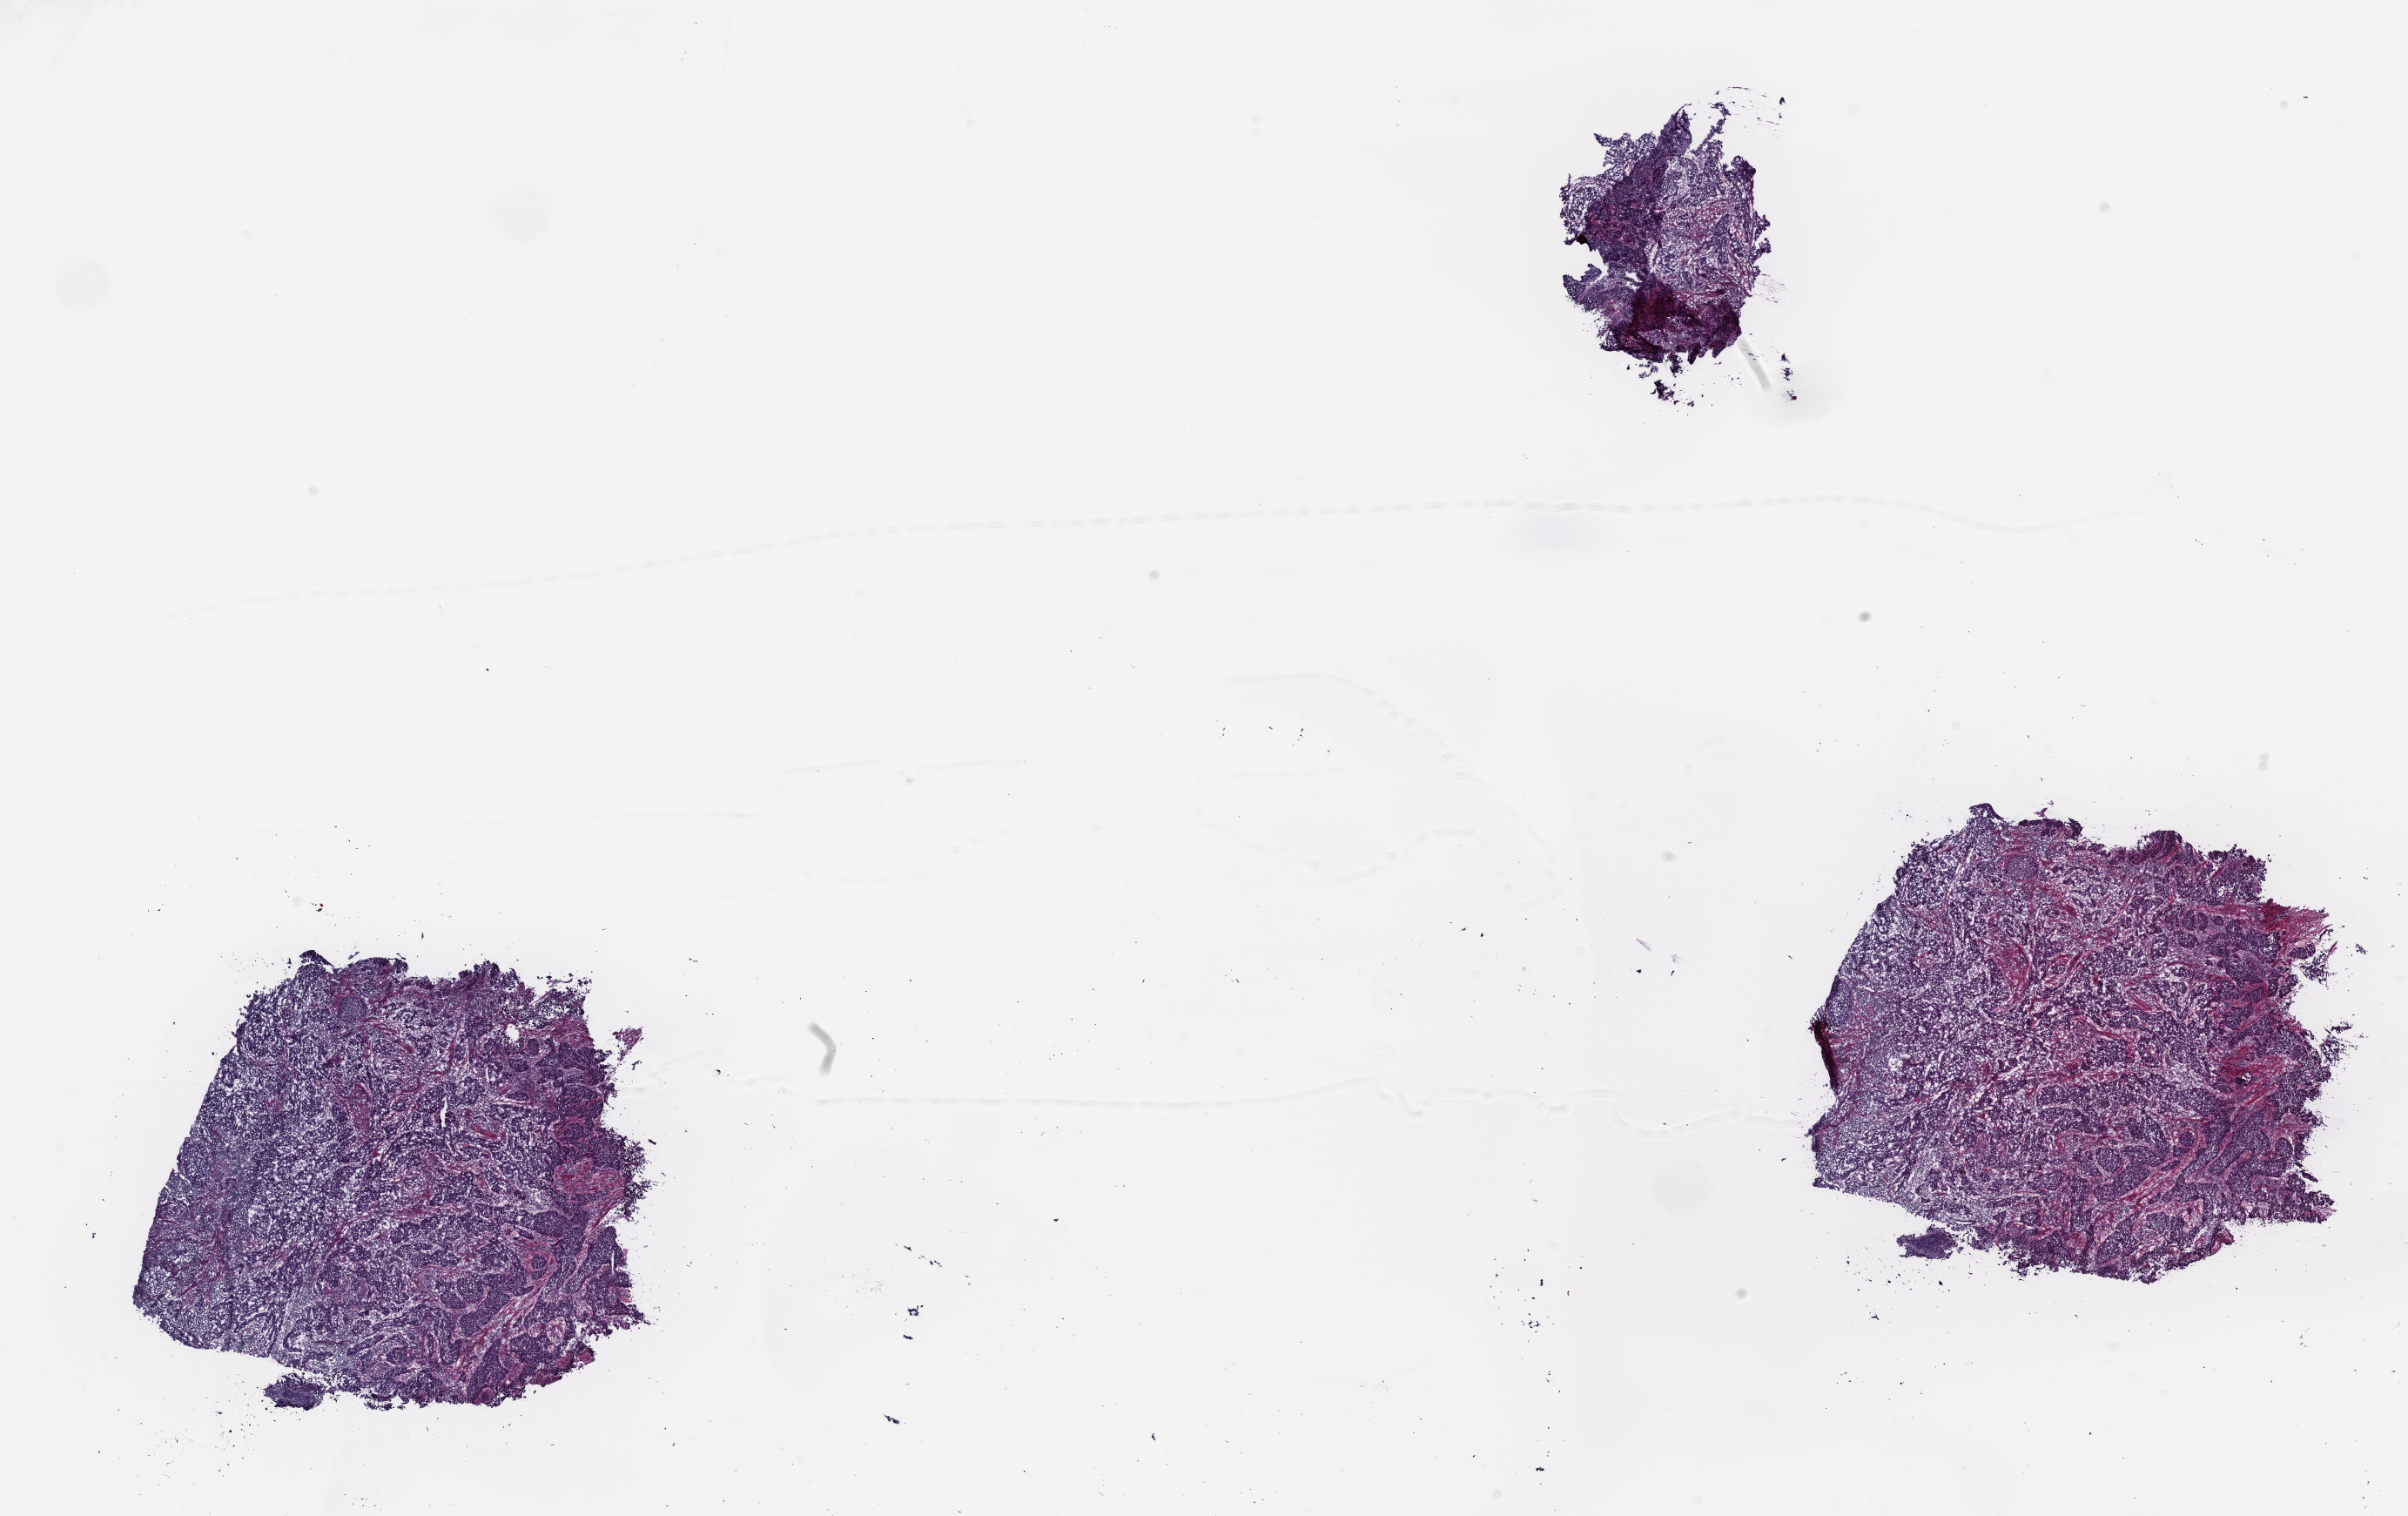
Digitized H&E tissue section (whole slide) — low-resolution overview of the scanned area, about 21.8 x 13.7 mm (acquisition: 40x scan). Frozen section from the top of the tissue portion. Primary tumour sample from the cervix. Patient: female, age at initial diagnosis 49 years.
Histologic diagnosis: Squamous cell carcinoma, NOS (cervix uteri).